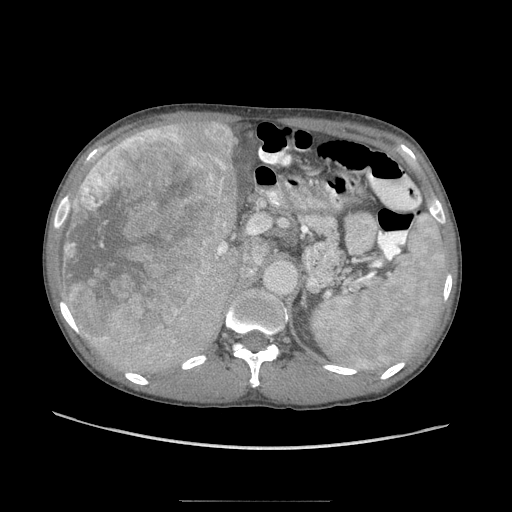
Contrast-enhanced abdominal CT (liver protocol), one axial slice. Slice 54 of 103 in the series (ordered by position). Reconstruction kernel STANDARD. 120 kVp. Soft-tissue window (W 400 / L 40 HU). 512 × 512 image matrix. Case-level facts recorded for this patient, not image findings: diagnosis: hepatocellular carcinoma (patient treated with transarterial chemoembolisation; whether this scan precedes or follows treatment is not stated here); TNM stage (as recorded): Stage-IIIA; Child-Pugh class: A; tumour size: 16 cm.
Structures marked on this image (semi-automatic segmentation, software-assisted and operator-edited):
- liver parenchyma outside the tumour (the mass and vessels are separate outlines, so this box may not span the whole liver): bounding box <60,120,240,378> (left, top, right, bottom; pixels)
- mass: <62,122,238,344>
- liver vessels: <127,138,219,258>